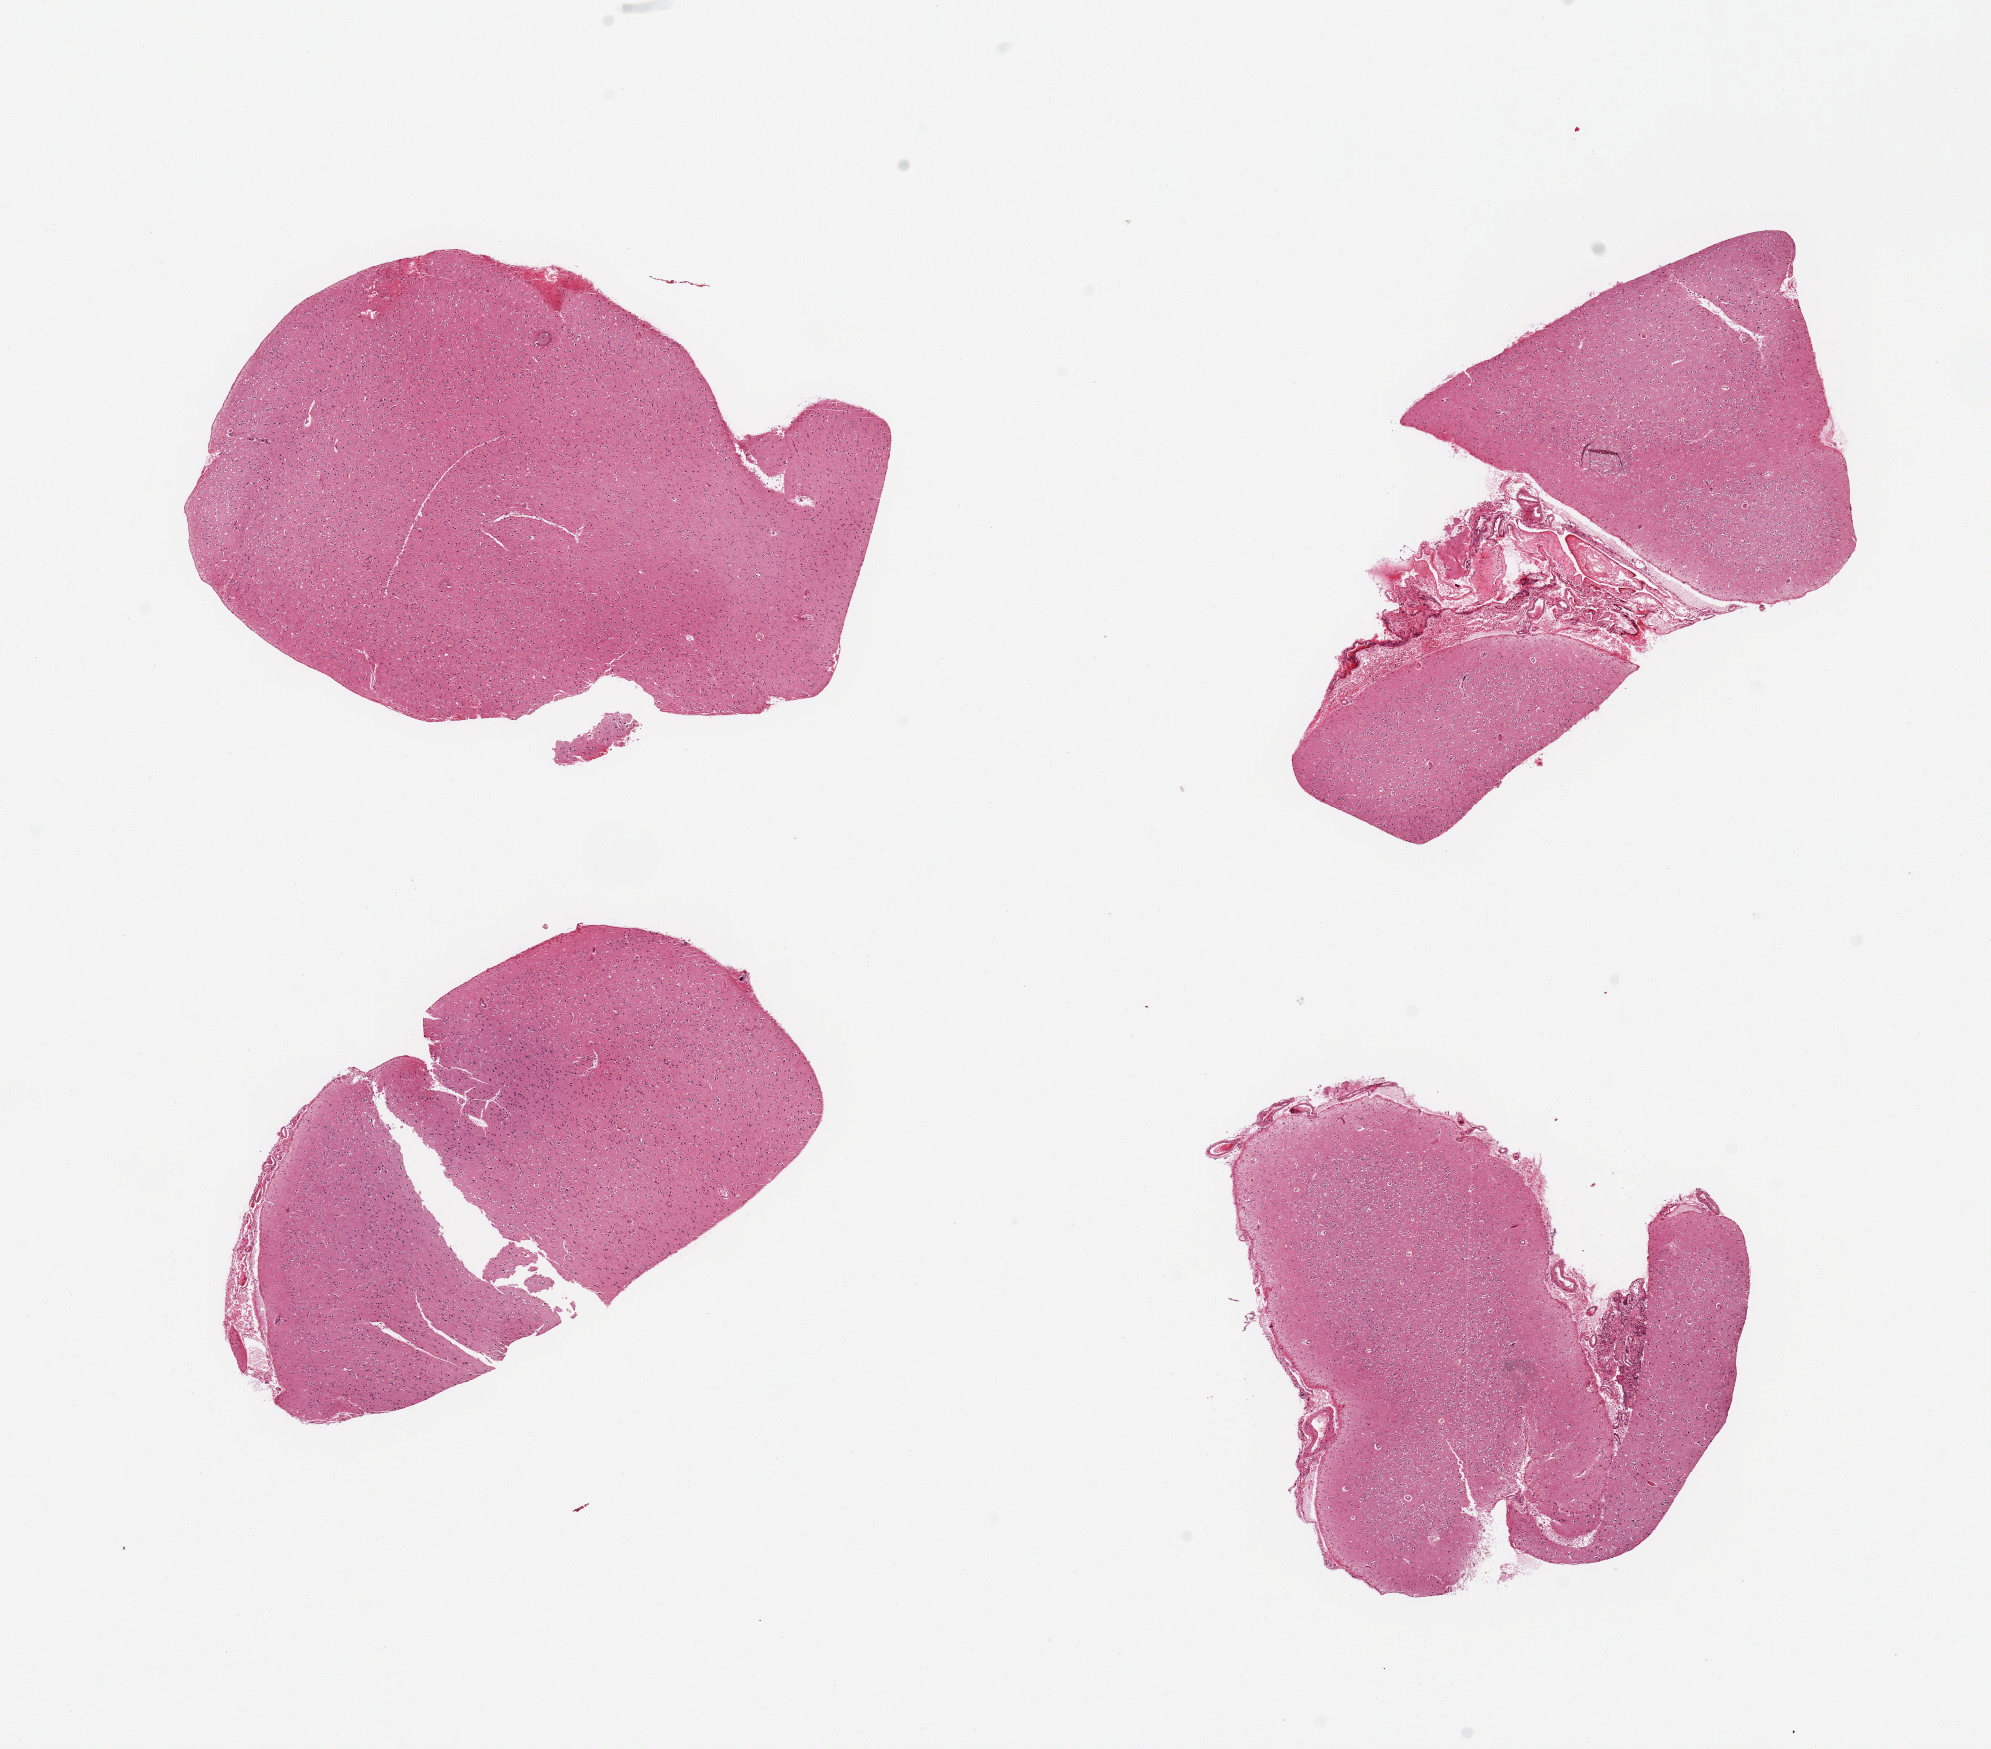
Whole-slide image, H&E stain, low-resolution overview of the scanned area, about 15.8 x 13.8 mm (from a 20x scan); PAXgene-fixed paraffin-embedded (PFPE) section; target tissue: cerebral cortex; donor tissue sample. Donor sex: female.
Reviewer comment on this tissue sample: 4 pieces, no abnormalities, ~10-15% contaminant dural elements/vessels.